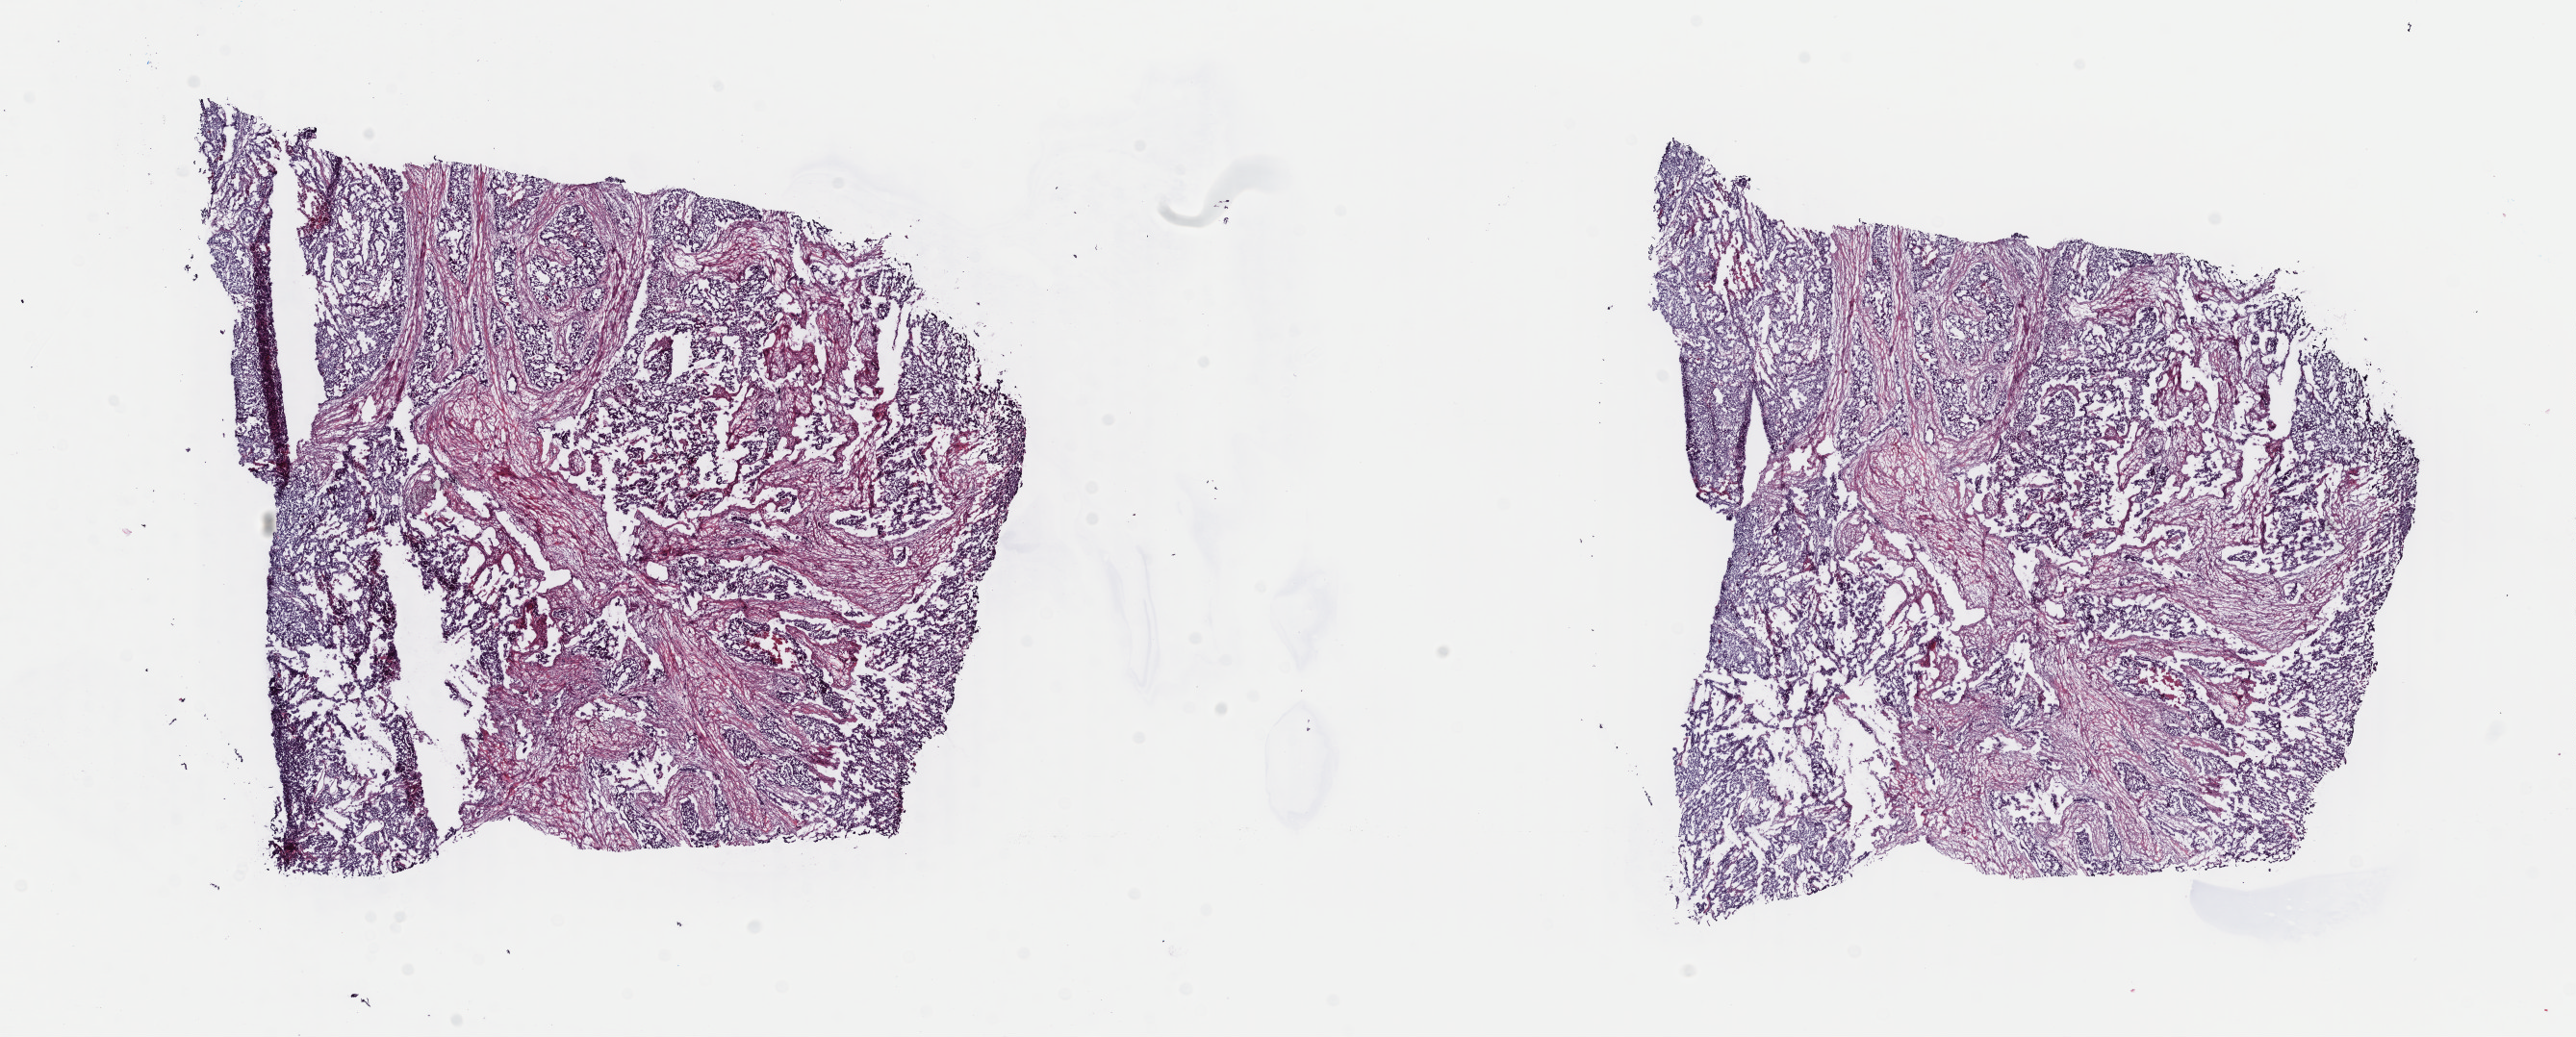
Hematoxylin and eosin (H&E) stained whole-slide image, shown as a low-resolution overview of the whole scanned area (about 21.1 x 8.5 mm, from a 40x scan). Frozen section from the top of the tissue portion. Primary tumour sample from the cervix. Female, age 38 years at initial diagnosis. Histologic grade: G3 (poorly differentiated). Pathologist review of this section (percent, as recorded): tumour cells 97%, tumour nuclei 75%, normal cells 0%, stromal cells 0%, necrosis 3%. Inflammatory infiltration, as recorded: lymphocyte infiltration 2%, monocyte infiltration 0%, neutrophil infiltration 0%.
FIGO stage: IB1. Lymph nodes positive (case pathology): 0 of 7 examined. Histologic diagnosis: Endometrioid adenocarcinoma, NOS (cervix uteri).